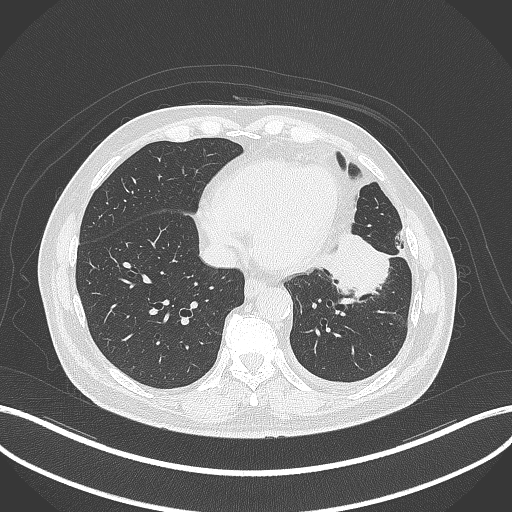
Chest CT, one axial slice; slice 113 of 230 in the series (ordered by position); reconstruction kernel B70f; lung window (W 1500 / L -600 HU); 1 mm slice thickness; 512 × 512 image matrix. Male patient, age 68 years. Case-level facts recorded for this patient, not image findings: clinical TNM (as recorded): T2b N0 M0.
Outlined on this slice (rectangle marked by the reading radiologist):
- lung tumour (recorded histology: squamous cell carcinoma): bounding box [x1, y1, x2, y2] px = [319, 226, 397, 302]